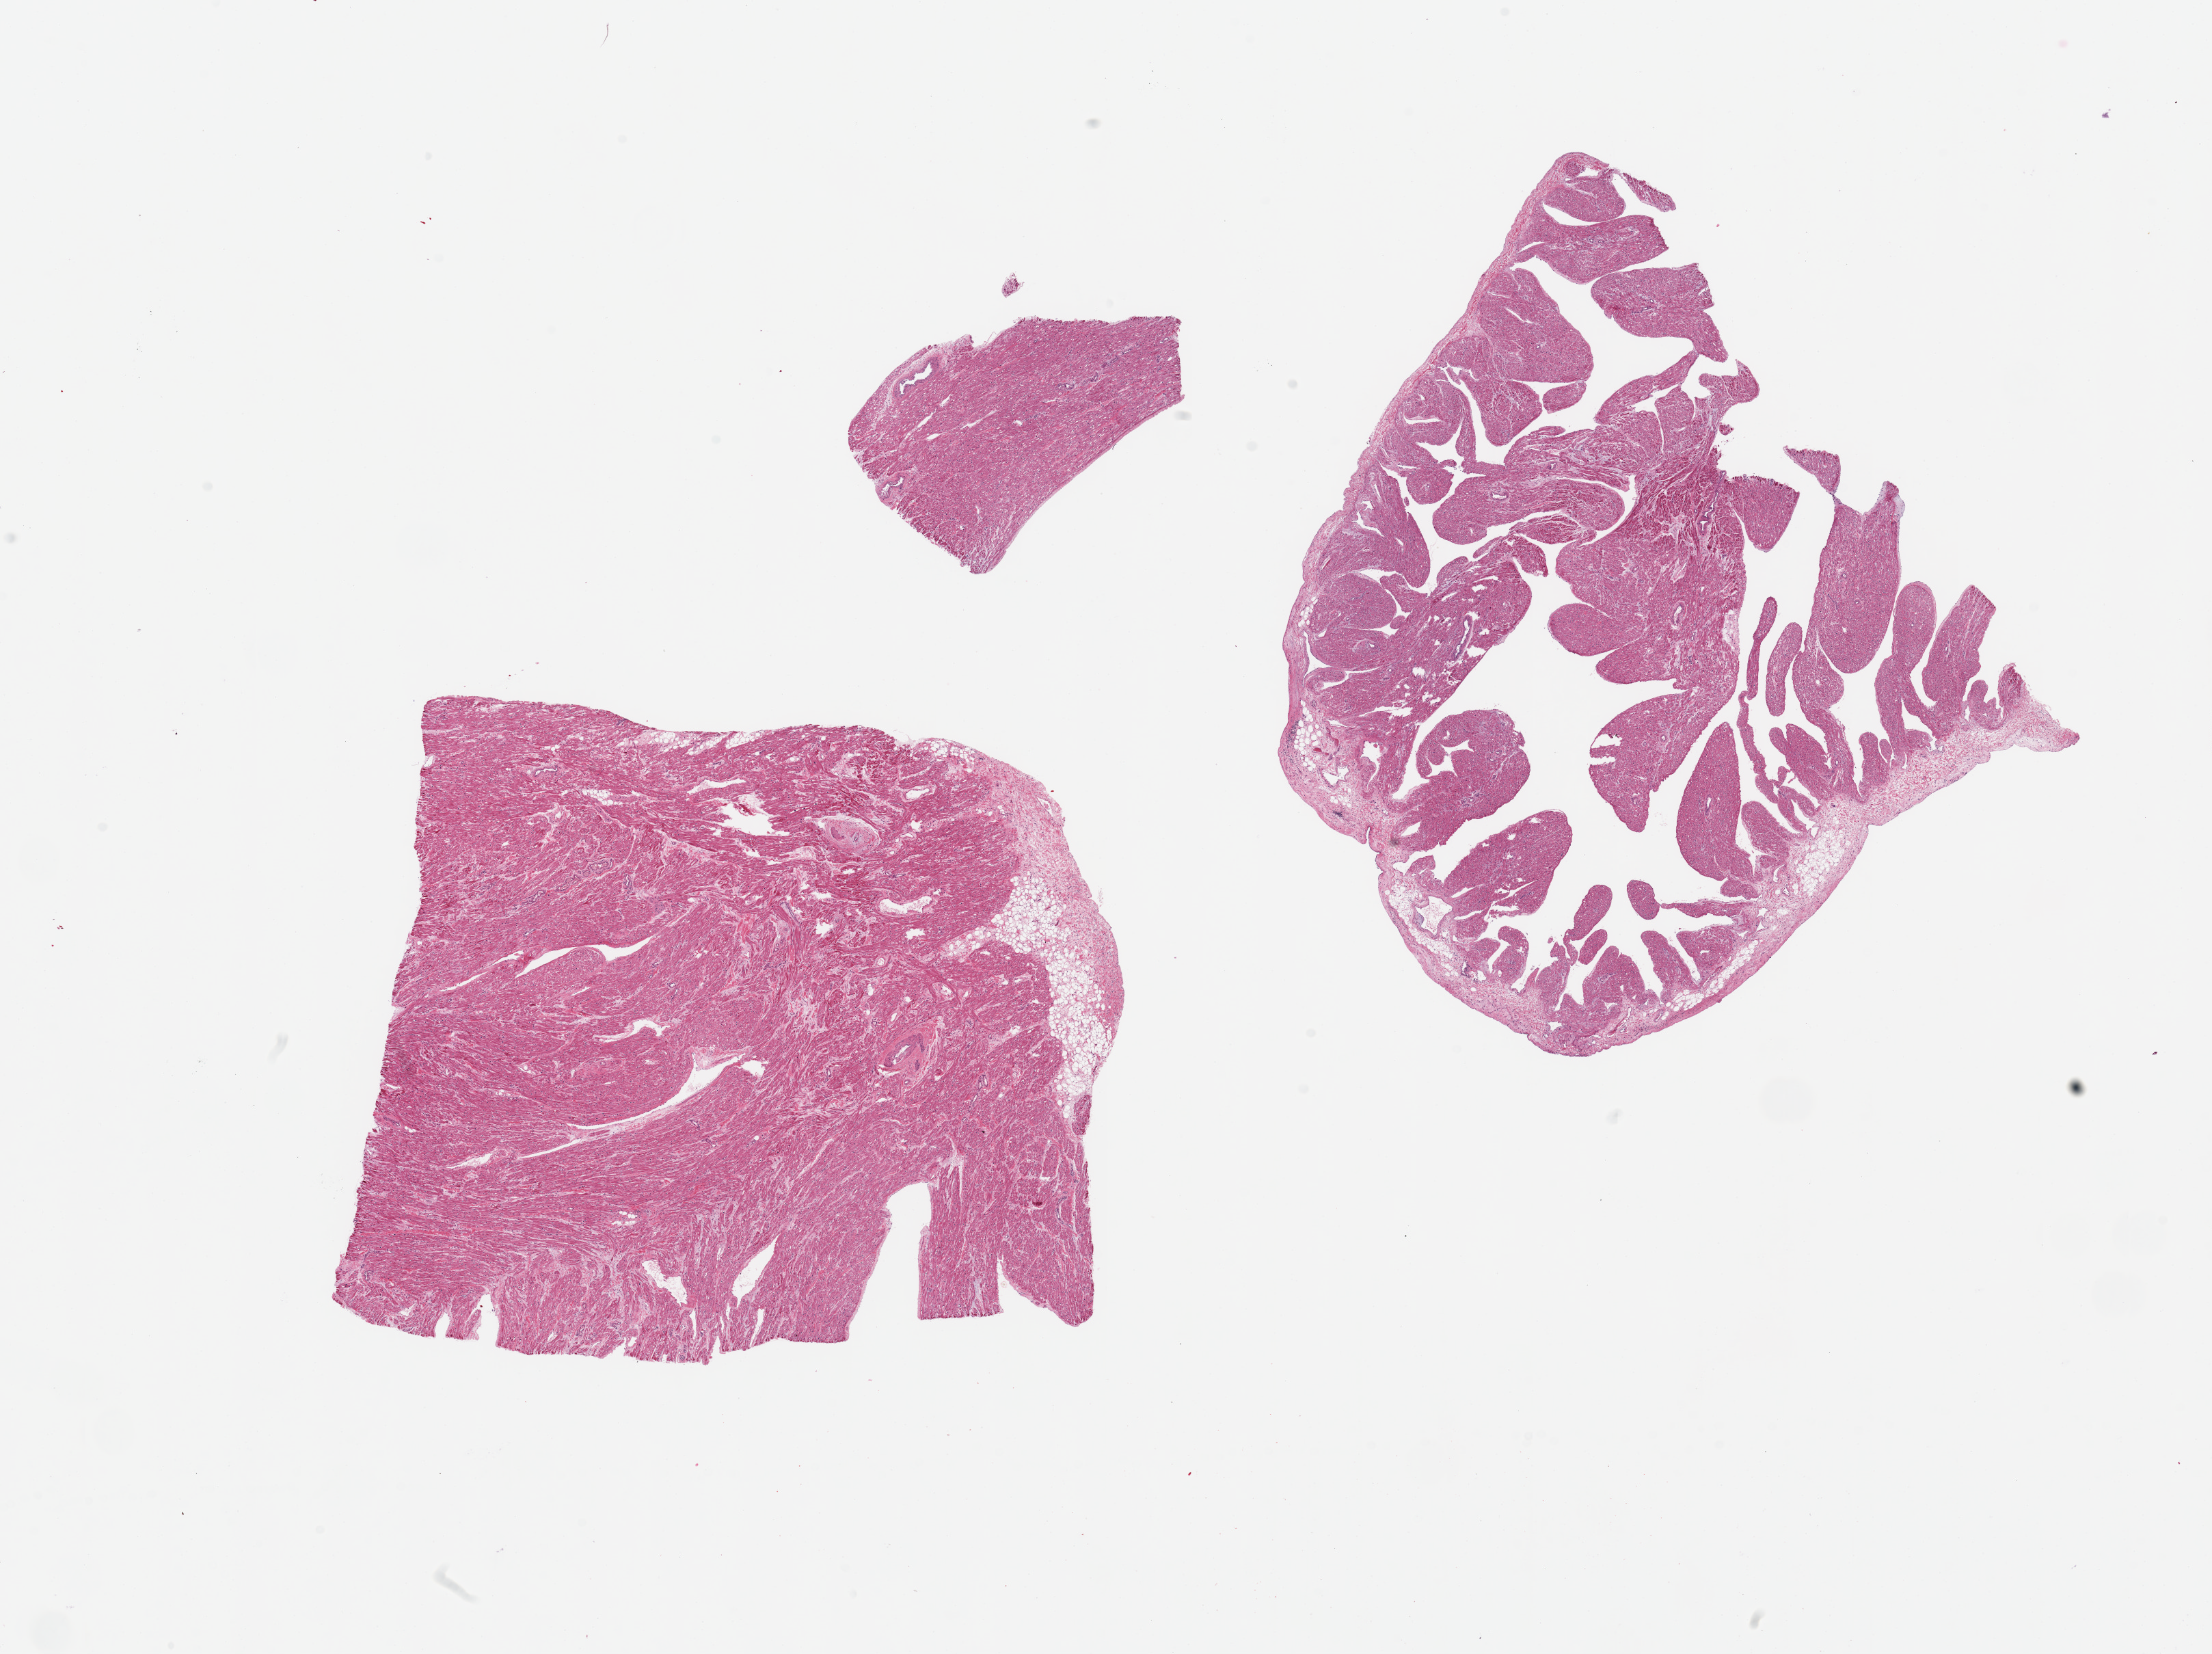
Whole-slide image, hematoxylin and eosin (H&E) stain, shown as a low-resolution overview of the whole scanned area (about 25.6 x 19.1 mm, from a 20x scan), PAXgene-fixed paraffin-embedded (PFPE) section, sampled site (target tissue): auricular appendage, tissue donor sample. Female donor.
Pathologist's review note for this sample: 3 pieces, up to 9x8mm.